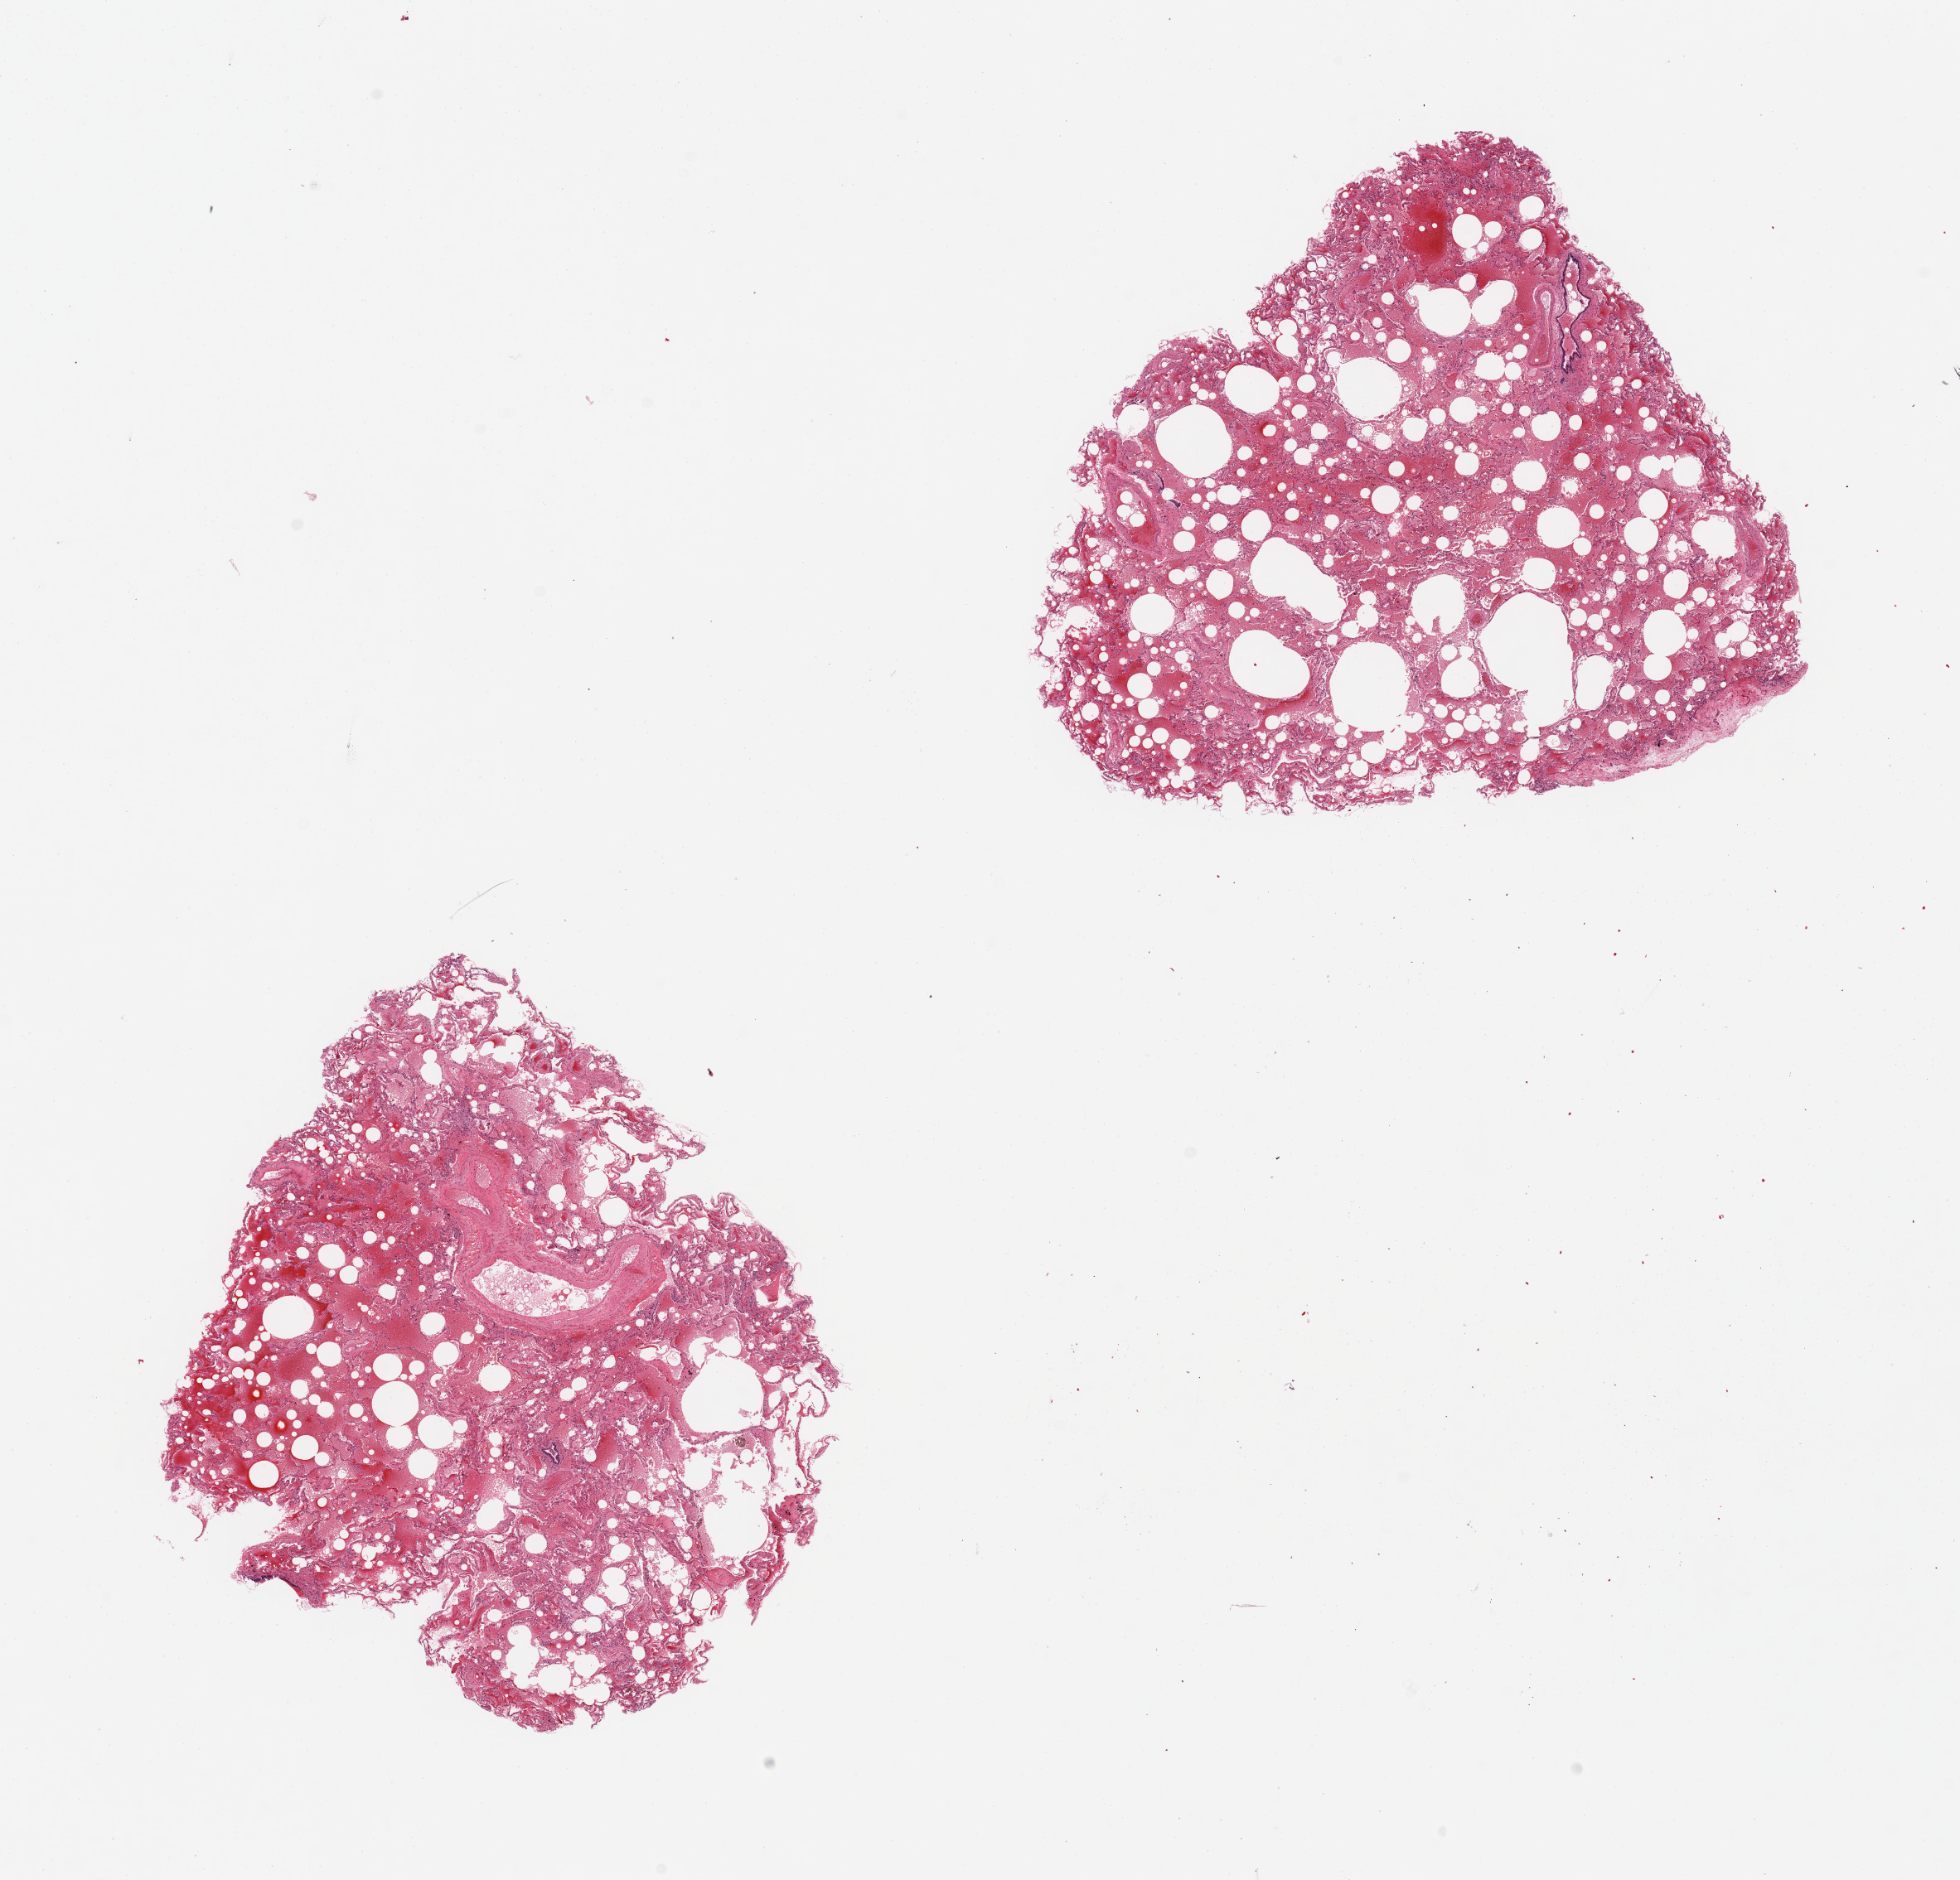
Haematoxylin and eosin whole-slide image — whole scanned area (about 18.7 x 17.9 mm) shown as a low-resolution overview, PAXgene-fixed, paraffin-embedded tissue, target tissue: lung, donor tissue sample.
Reviewer comment on this tissue sample: 2 pieces, marked congestion, ? emphysemaotus changes.